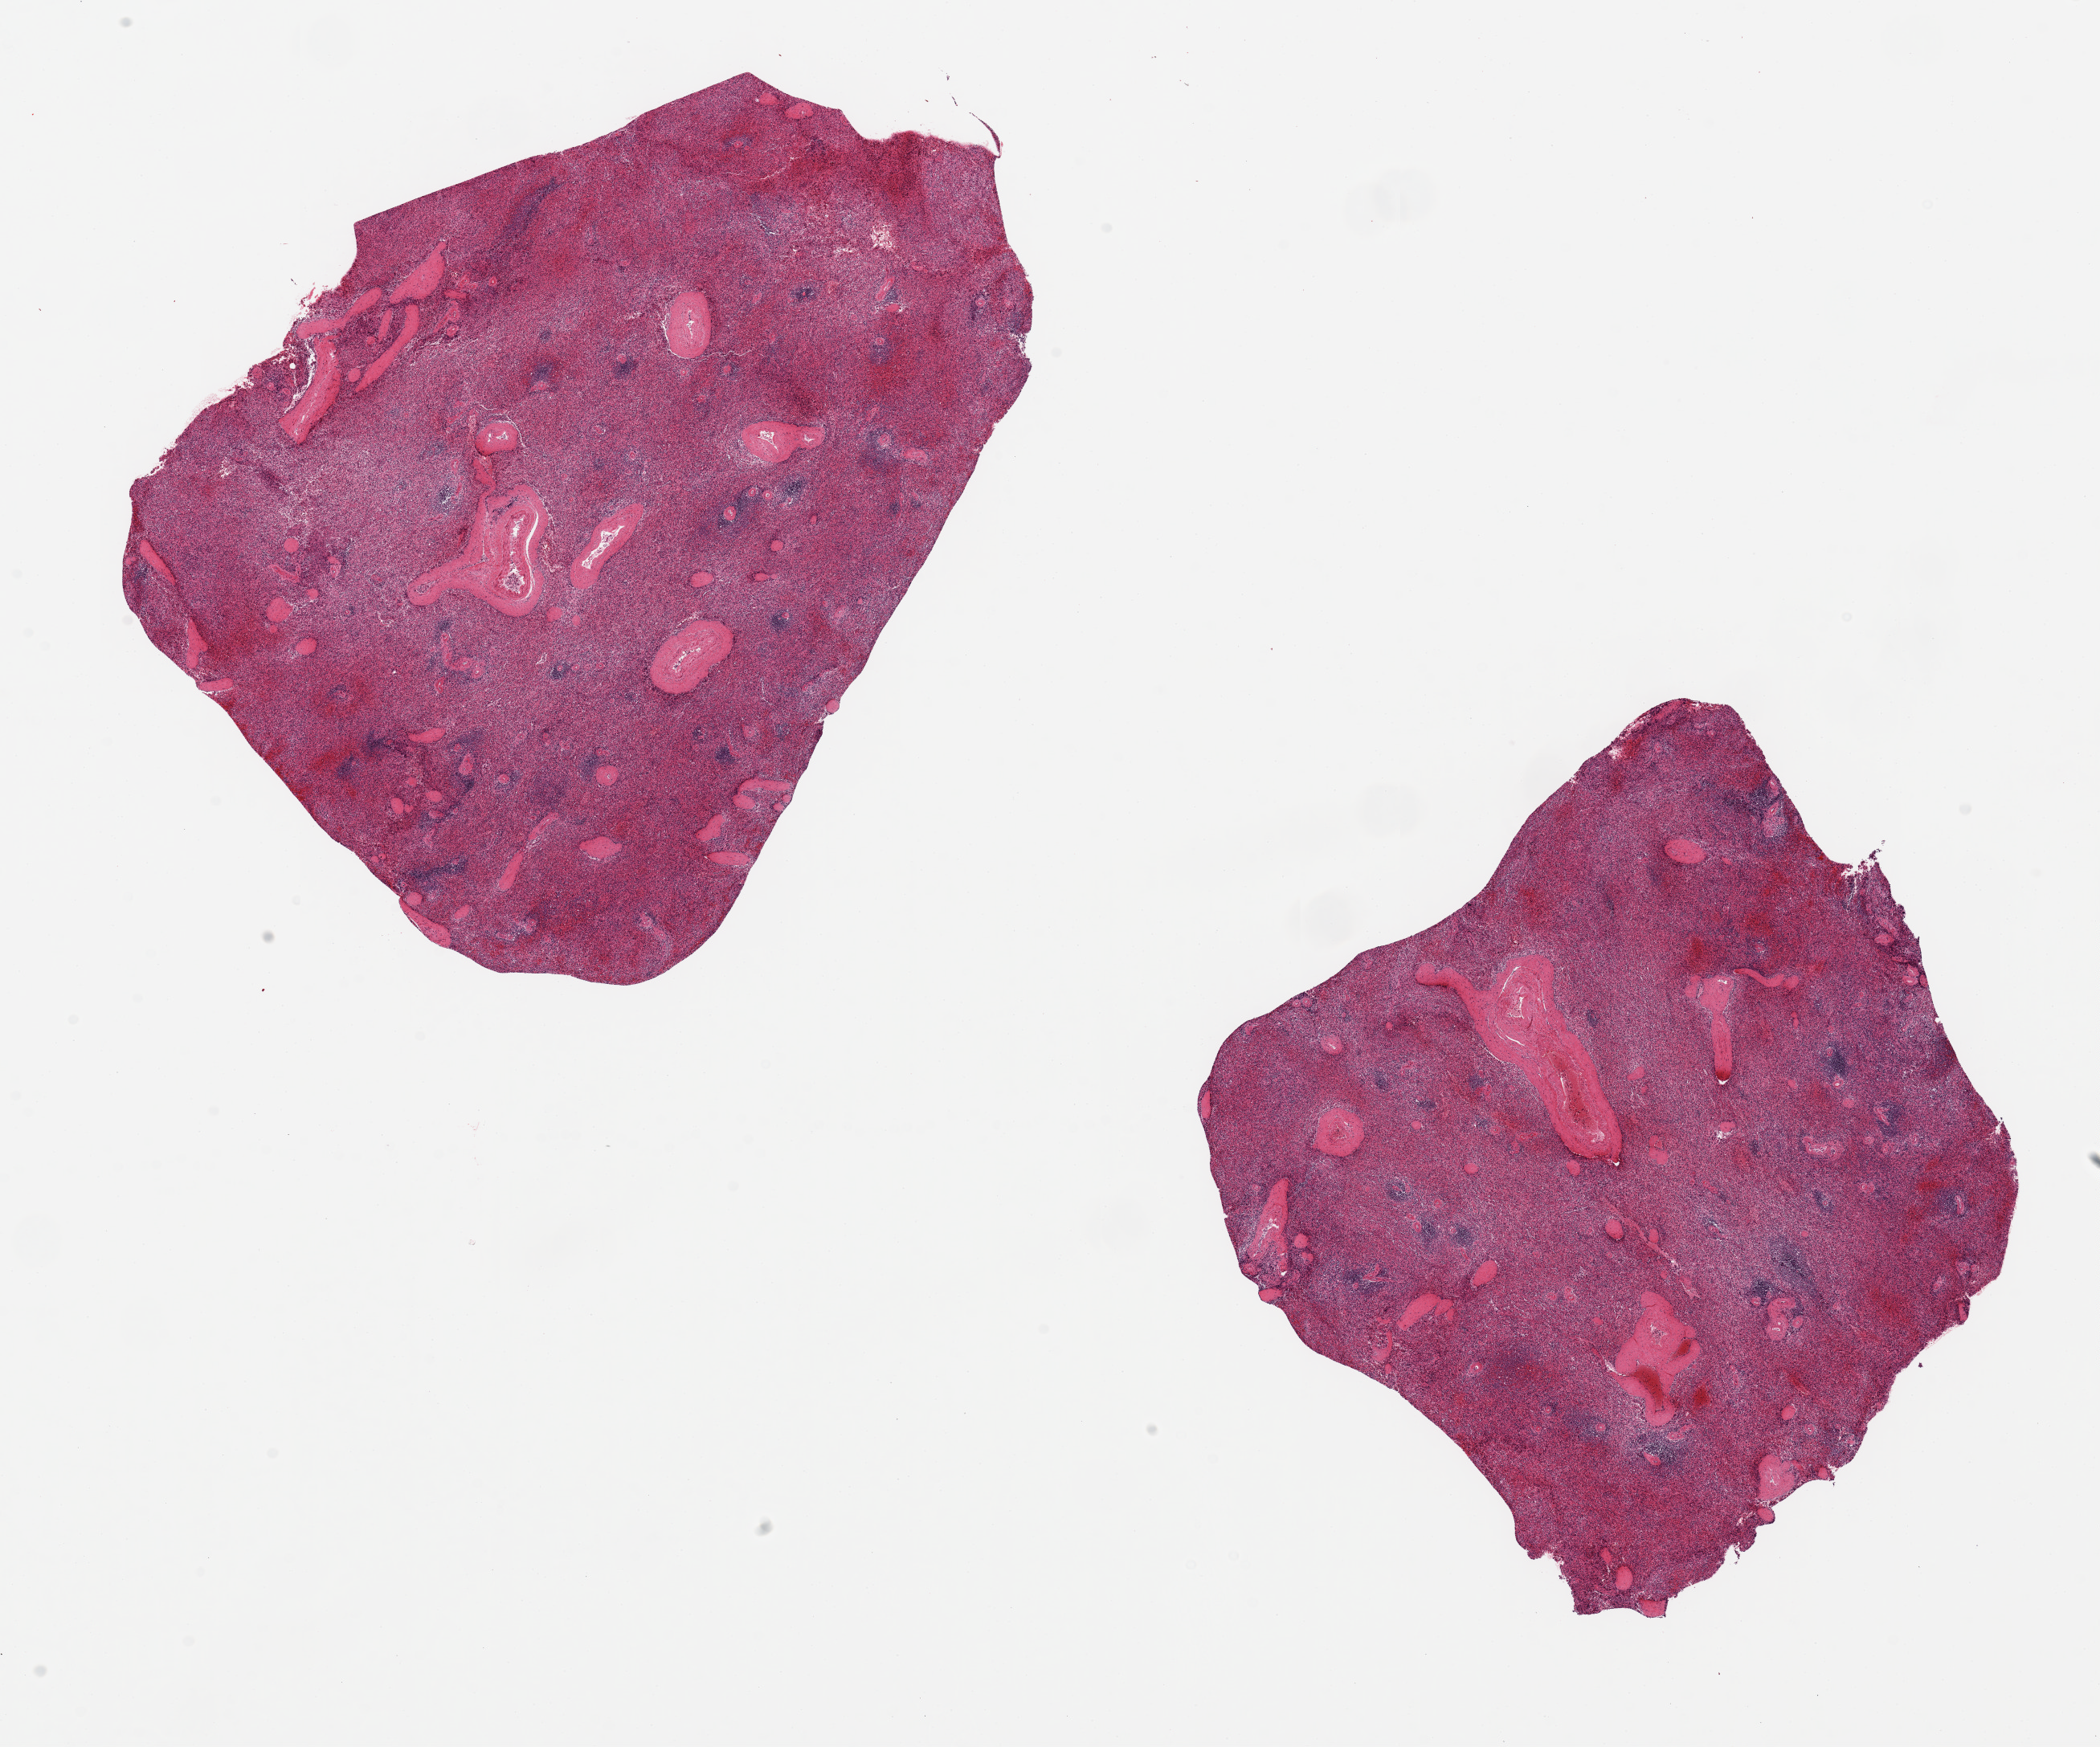
Whole-slide image, H&E stain — whole scanned area (about 20.7 x 17.2 mm, slide scanned at 20x) shown as a low-resolution overview. PAXgene-fixed paraffin-embedded (PFPE) section. Sampled site (target tissue): spleen. Tissue donor sample.
Reviewer comment on this tissue sample: 2 pieces ~8x6mm, congested.